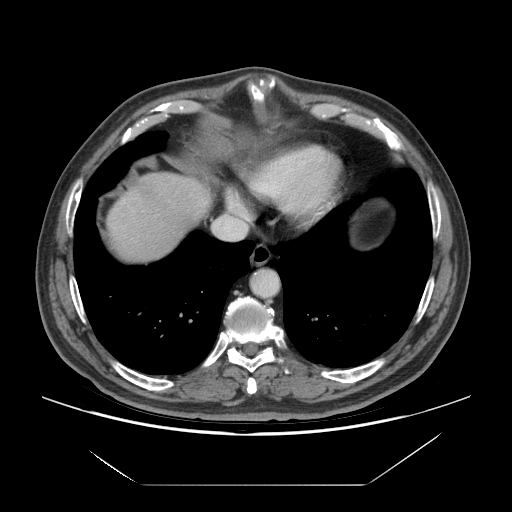
Contrast-enhanced abdominal CT (liver protocol), one axial slice. Position 65 of 75 along the scan axis. Reconstruction kernel STANDARD. 140 kVp. Soft-tissue window (W 400 / L 40 HU). 512 × 512 image matrix, field of view 420 × 420 mm. From the clinical record (not read from this slice): diagnosis: hepatocellular carcinoma (patient treated with transarterial chemoembolisation; whether this scan precedes or follows treatment is not stated here); TNM stage (as recorded): Stage-I; Child-Pugh class: A; tumour differentiation: well differentiated; tumour nodularity: uninodular.
Outlined on this slice (semi-automatic segmentation, software-assisted and operator-edited):
- liver parenchyma outside the tumour (the mass and vessels are separate outlines, so this box may not span the whole liver): box from (x=108, y=172) to (x=212, y=260) px